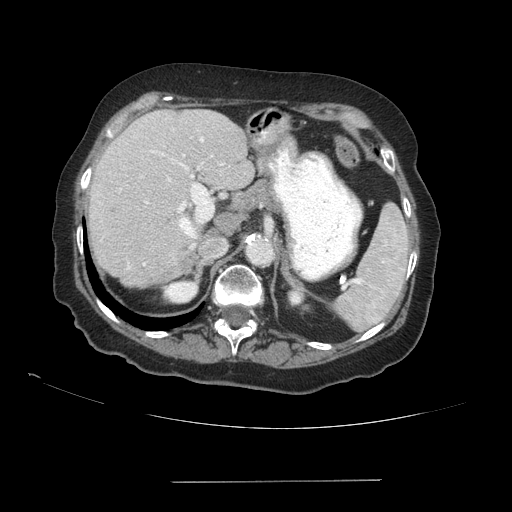
Contrast-enhanced abdominal CT (liver protocol), one axial slice; position 61 of 89 along the scan axis; 140 kVp; soft-tissue window (W 400 / L 40 HU); 2.5 mm slice thickness; 512 × 512 image matrix. From the clinical record (not read from this slice): diagnosis: hepatocellular carcinoma (patient treated with transarterial chemoembolisation; whether this scan precedes or follows treatment is not stated here); TNM stage (as recorded): Stage-IVA; Child-Pugh class: A.
Annotated regions visible in this slice (semi-automatically segmented with operator editing):
- liver parenchyma outside the tumour (the mass and vessels are separate outlines, so this box may not span the whole liver): box from (x=88, y=110) to (x=254, y=288) px
- liver vessels: (x=128, y=137)–(x=224, y=269)